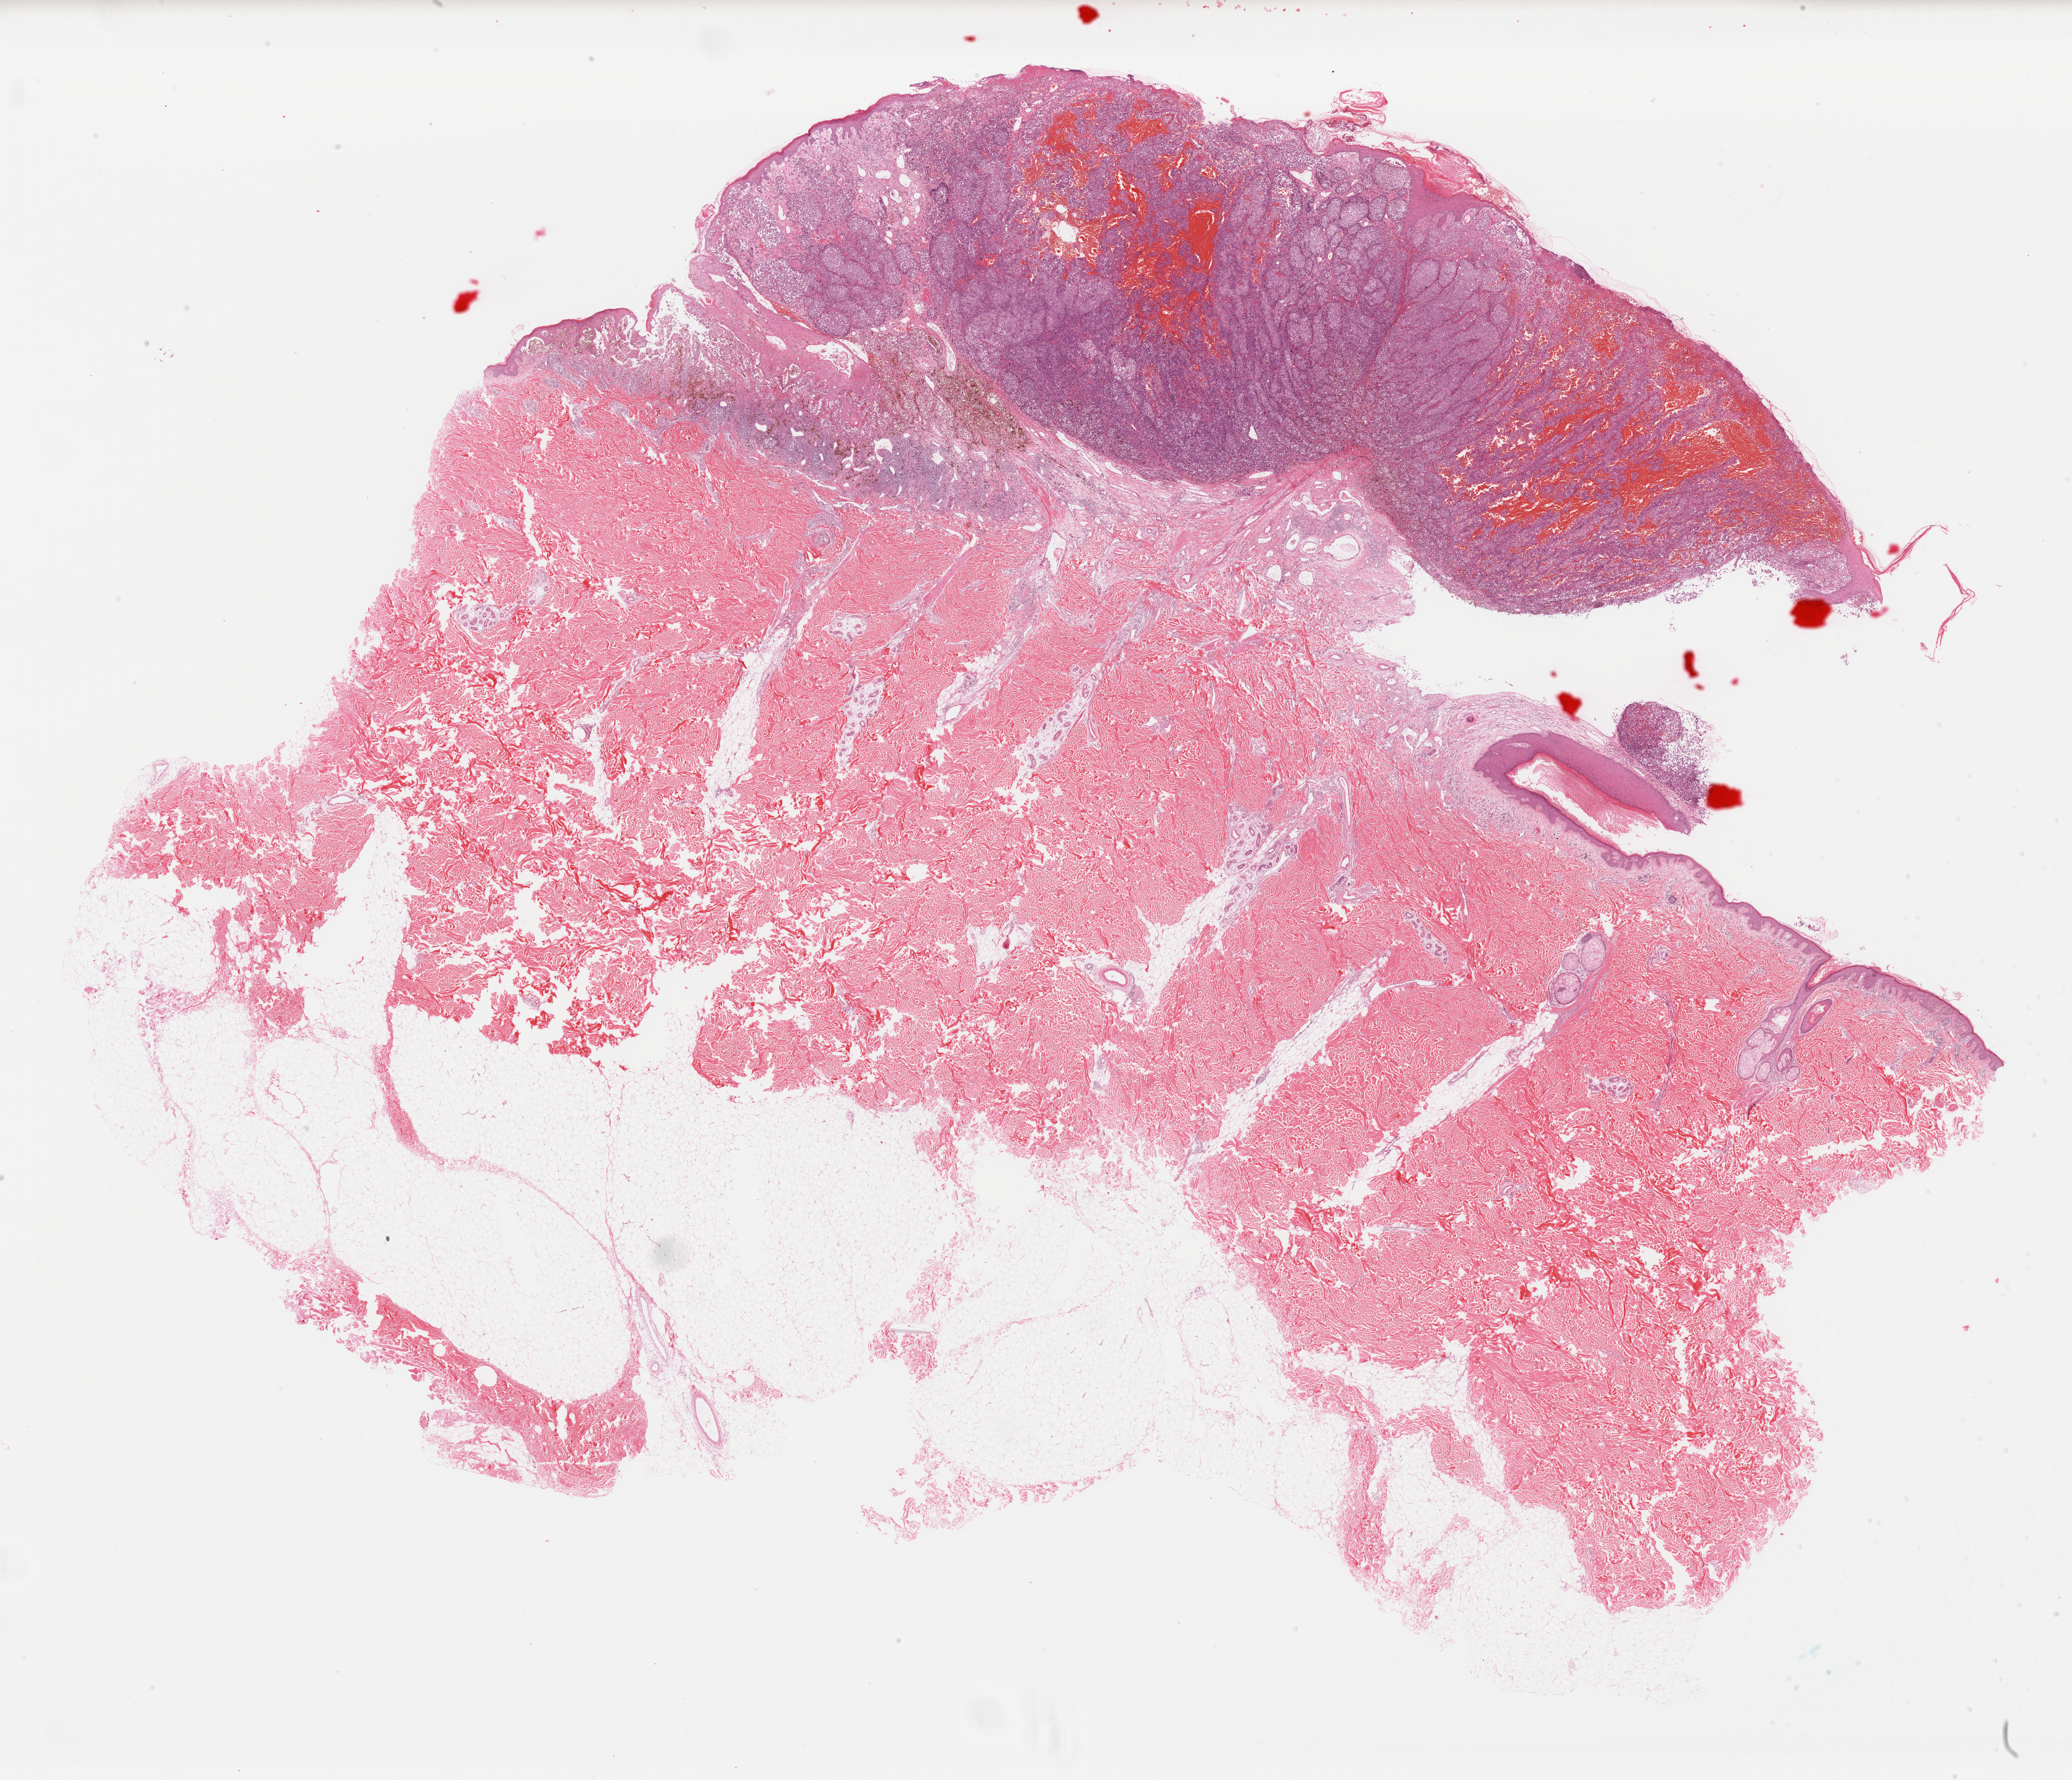
Hematoxylin and eosin (H&E) stained whole-slide image, low-resolution overview of the scanned area, about 26.5 x 22.8 mm, formalin-fixed paraffin-embedded (FFPE) diagnostic section, skin, primary tumour sample. Patient: male, age at initial diagnosis 57 years.
AJCC pathologic stage: IIC. Diagnosis: Malignant melanoma, NOS.